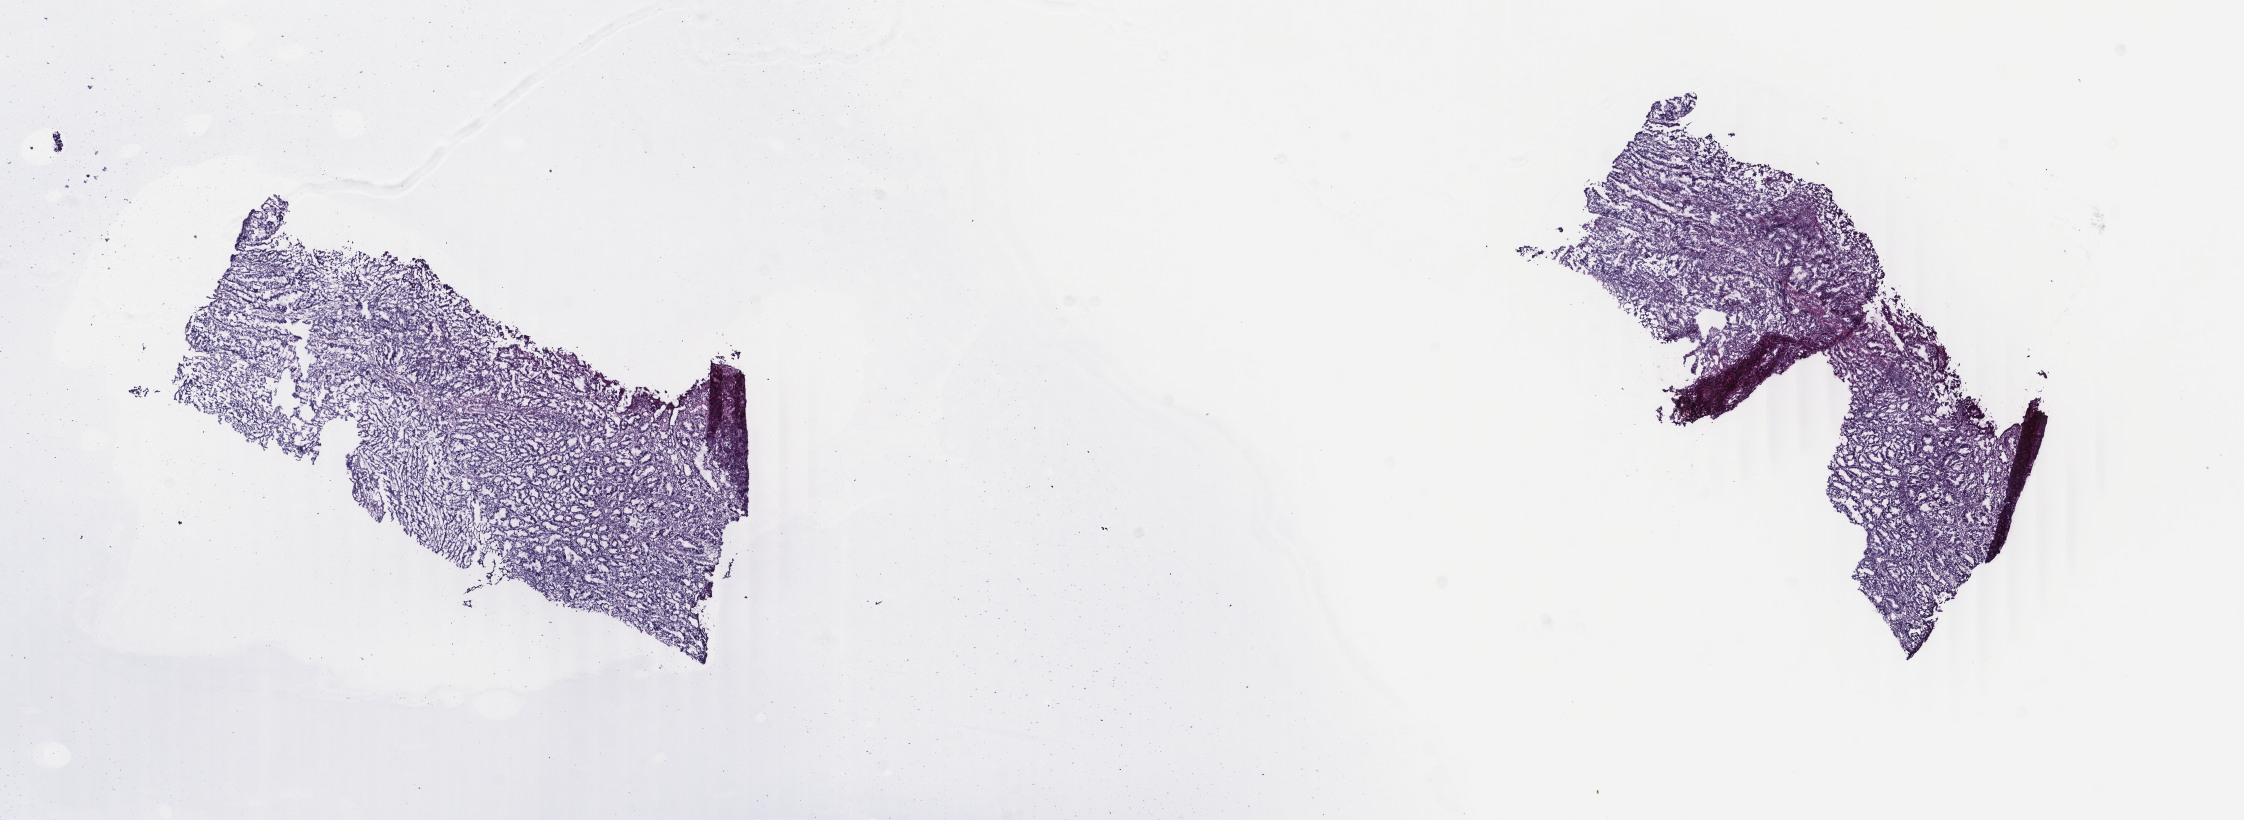
H&E whole-slide image, whole scanned area (about 17.8 x 6.5 mm) shown as a low-resolution overview, frozen section, uterus, primary tumour sample. Female patient; age at initial diagnosis 51 years.
Pathologic diagnosis: Endometrioid adenocarcinoma, NOS (endometrium).